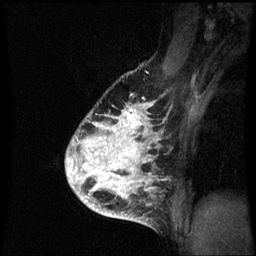
Breast MRI (dynamic contrast-enhanced), one sagittal slice; slice 48 of 60 in the series (ordered by position); dynamic contrast-enhanced series, image 2 of 3 at this slice position (ordered by acquisition); 1.5 T; TE 4.2 ms, TR 8.9 ms; 2 mm slice thickness; 256 × 256 image matrix, field of view 200 × 200 mm. Female patient, age 35 years. Case-level facts recorded for this patient, not image findings: setting: breast cancer imaged before/during neoadjuvant chemotherapy; receptor status: HR-positive, HER2-negative.
Outlined on this slice (semi-automatic segmentation, software-assisted and operator-edited):
- analysis volume of interest (the breast-tissue region the enhancement analysis was run in; not a lesion): box from (x=67, y=100) to (x=165, y=215) px
- tumour enhancement mask (voxels above the 70 % enhancement threshold inside the analysis volume of interest): (x=67, y=104)–(x=158, y=215)